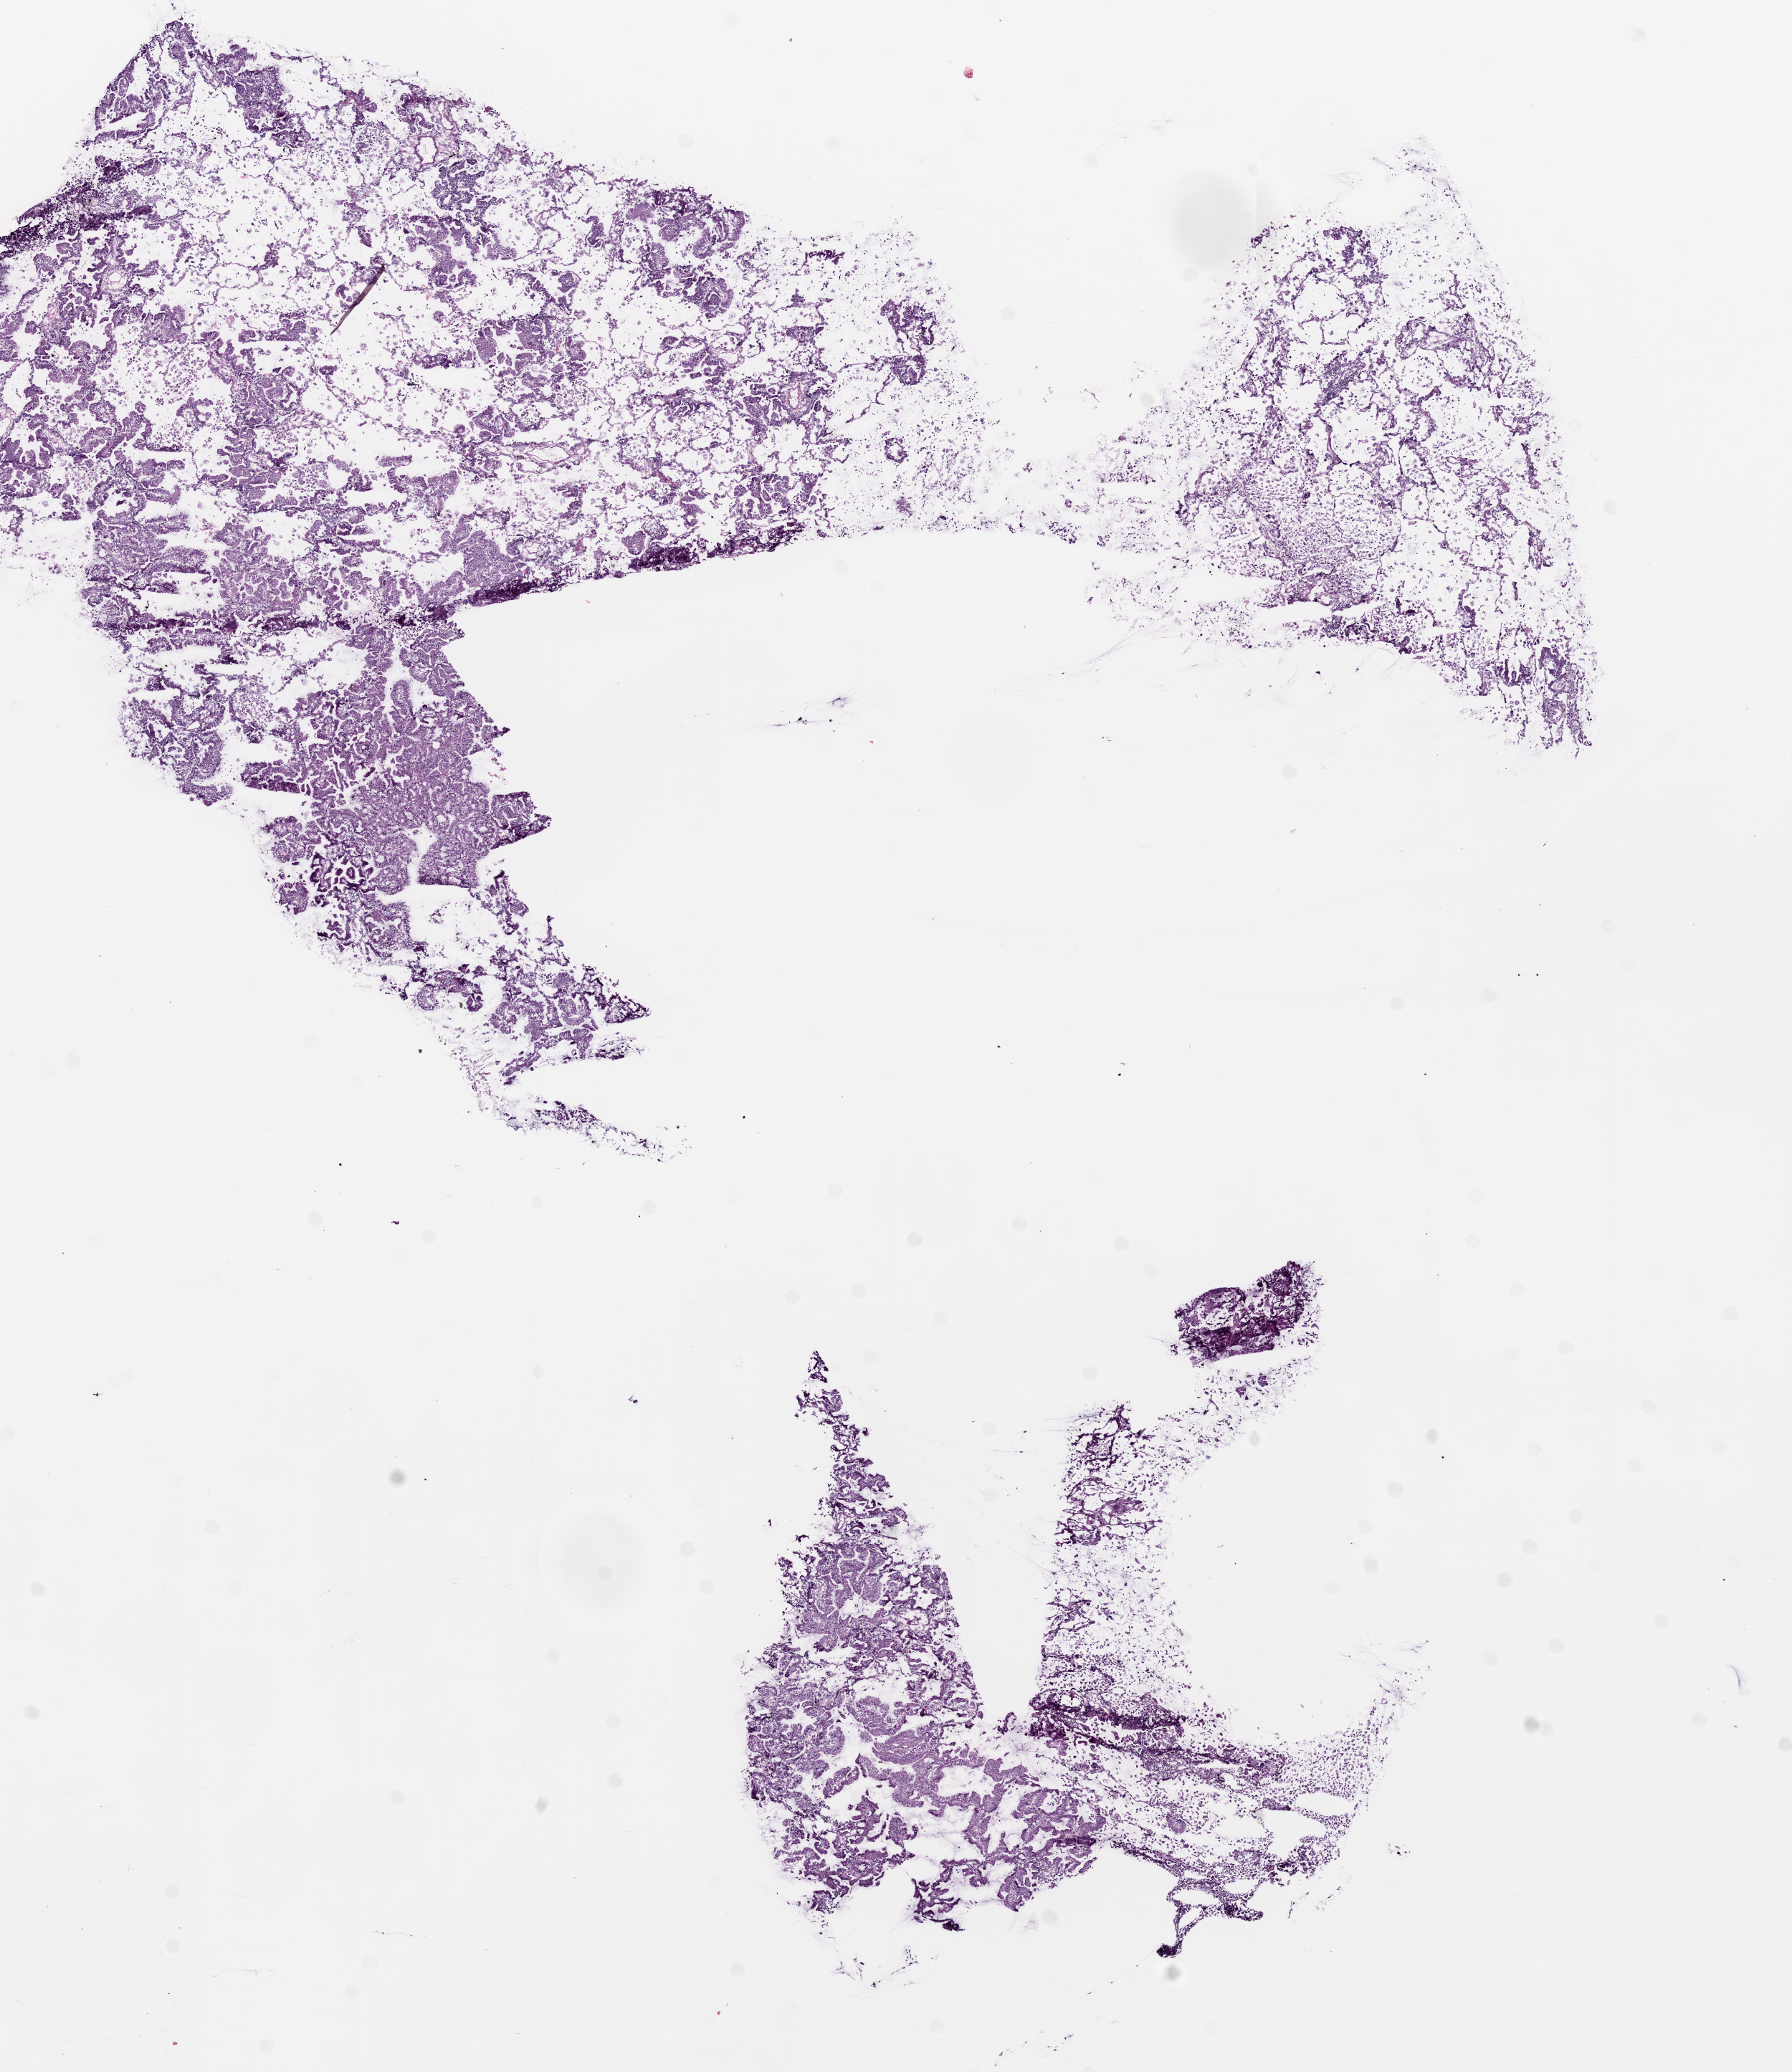
Digitized H&E-stained tissue section (whole slide), whole scanned area (about 10.0 x 11.6 mm, acquisition: 20x scan) shown as a low-resolution overview. Frozen section from the bottom of the tissue portion. Lung, primary tumour sample. Male patient; age at initial diagnosis 82 years. Pathologist review of this section (percent, as recorded): tumour cells 65%, tumour nuclei 60%, normal cells 25%, stromal cells 10%, necrosis 0%.
- TNM: T2 N0 M0
- histologic diagnosis: Adenocarcinoma with mixed subtypes
- AJCC pathologic stage: IB (6th edition)
- laterality: left